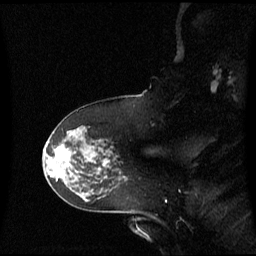
Breast MRI (dynamic contrast-enhanced), one sagittal slice. Position 42 of 60 along the scan axis. Dynamic contrast-enhanced series, image 2 of 3 at this slice position (ordered by acquisition). 1.5 T. TE 4.2 ms, TR 8.4 ms. 2.3 mm slice thickness. 256 × 256 image matrix, field of view 260 × 260 mm. Female patient, age 60 years. Case-level facts recorded for this patient, not image findings: setting: breast cancer imaged before/during neoadjuvant chemotherapy; receptor status: HR-positive, HER2-negative.
Annotated regions visible in this slice (semi-automatic segmentation, software-assisted and operator-edited):
- analysis volume of interest (the breast-tissue region the enhancement analysis was run in; not a lesion): bounding box <46,141,82,171> (left, top, right, bottom; pixels)
- tumour enhancement mask (voxels above the 70 % enhancement threshold inside the analysis volume of interest): <60,153,68,156>